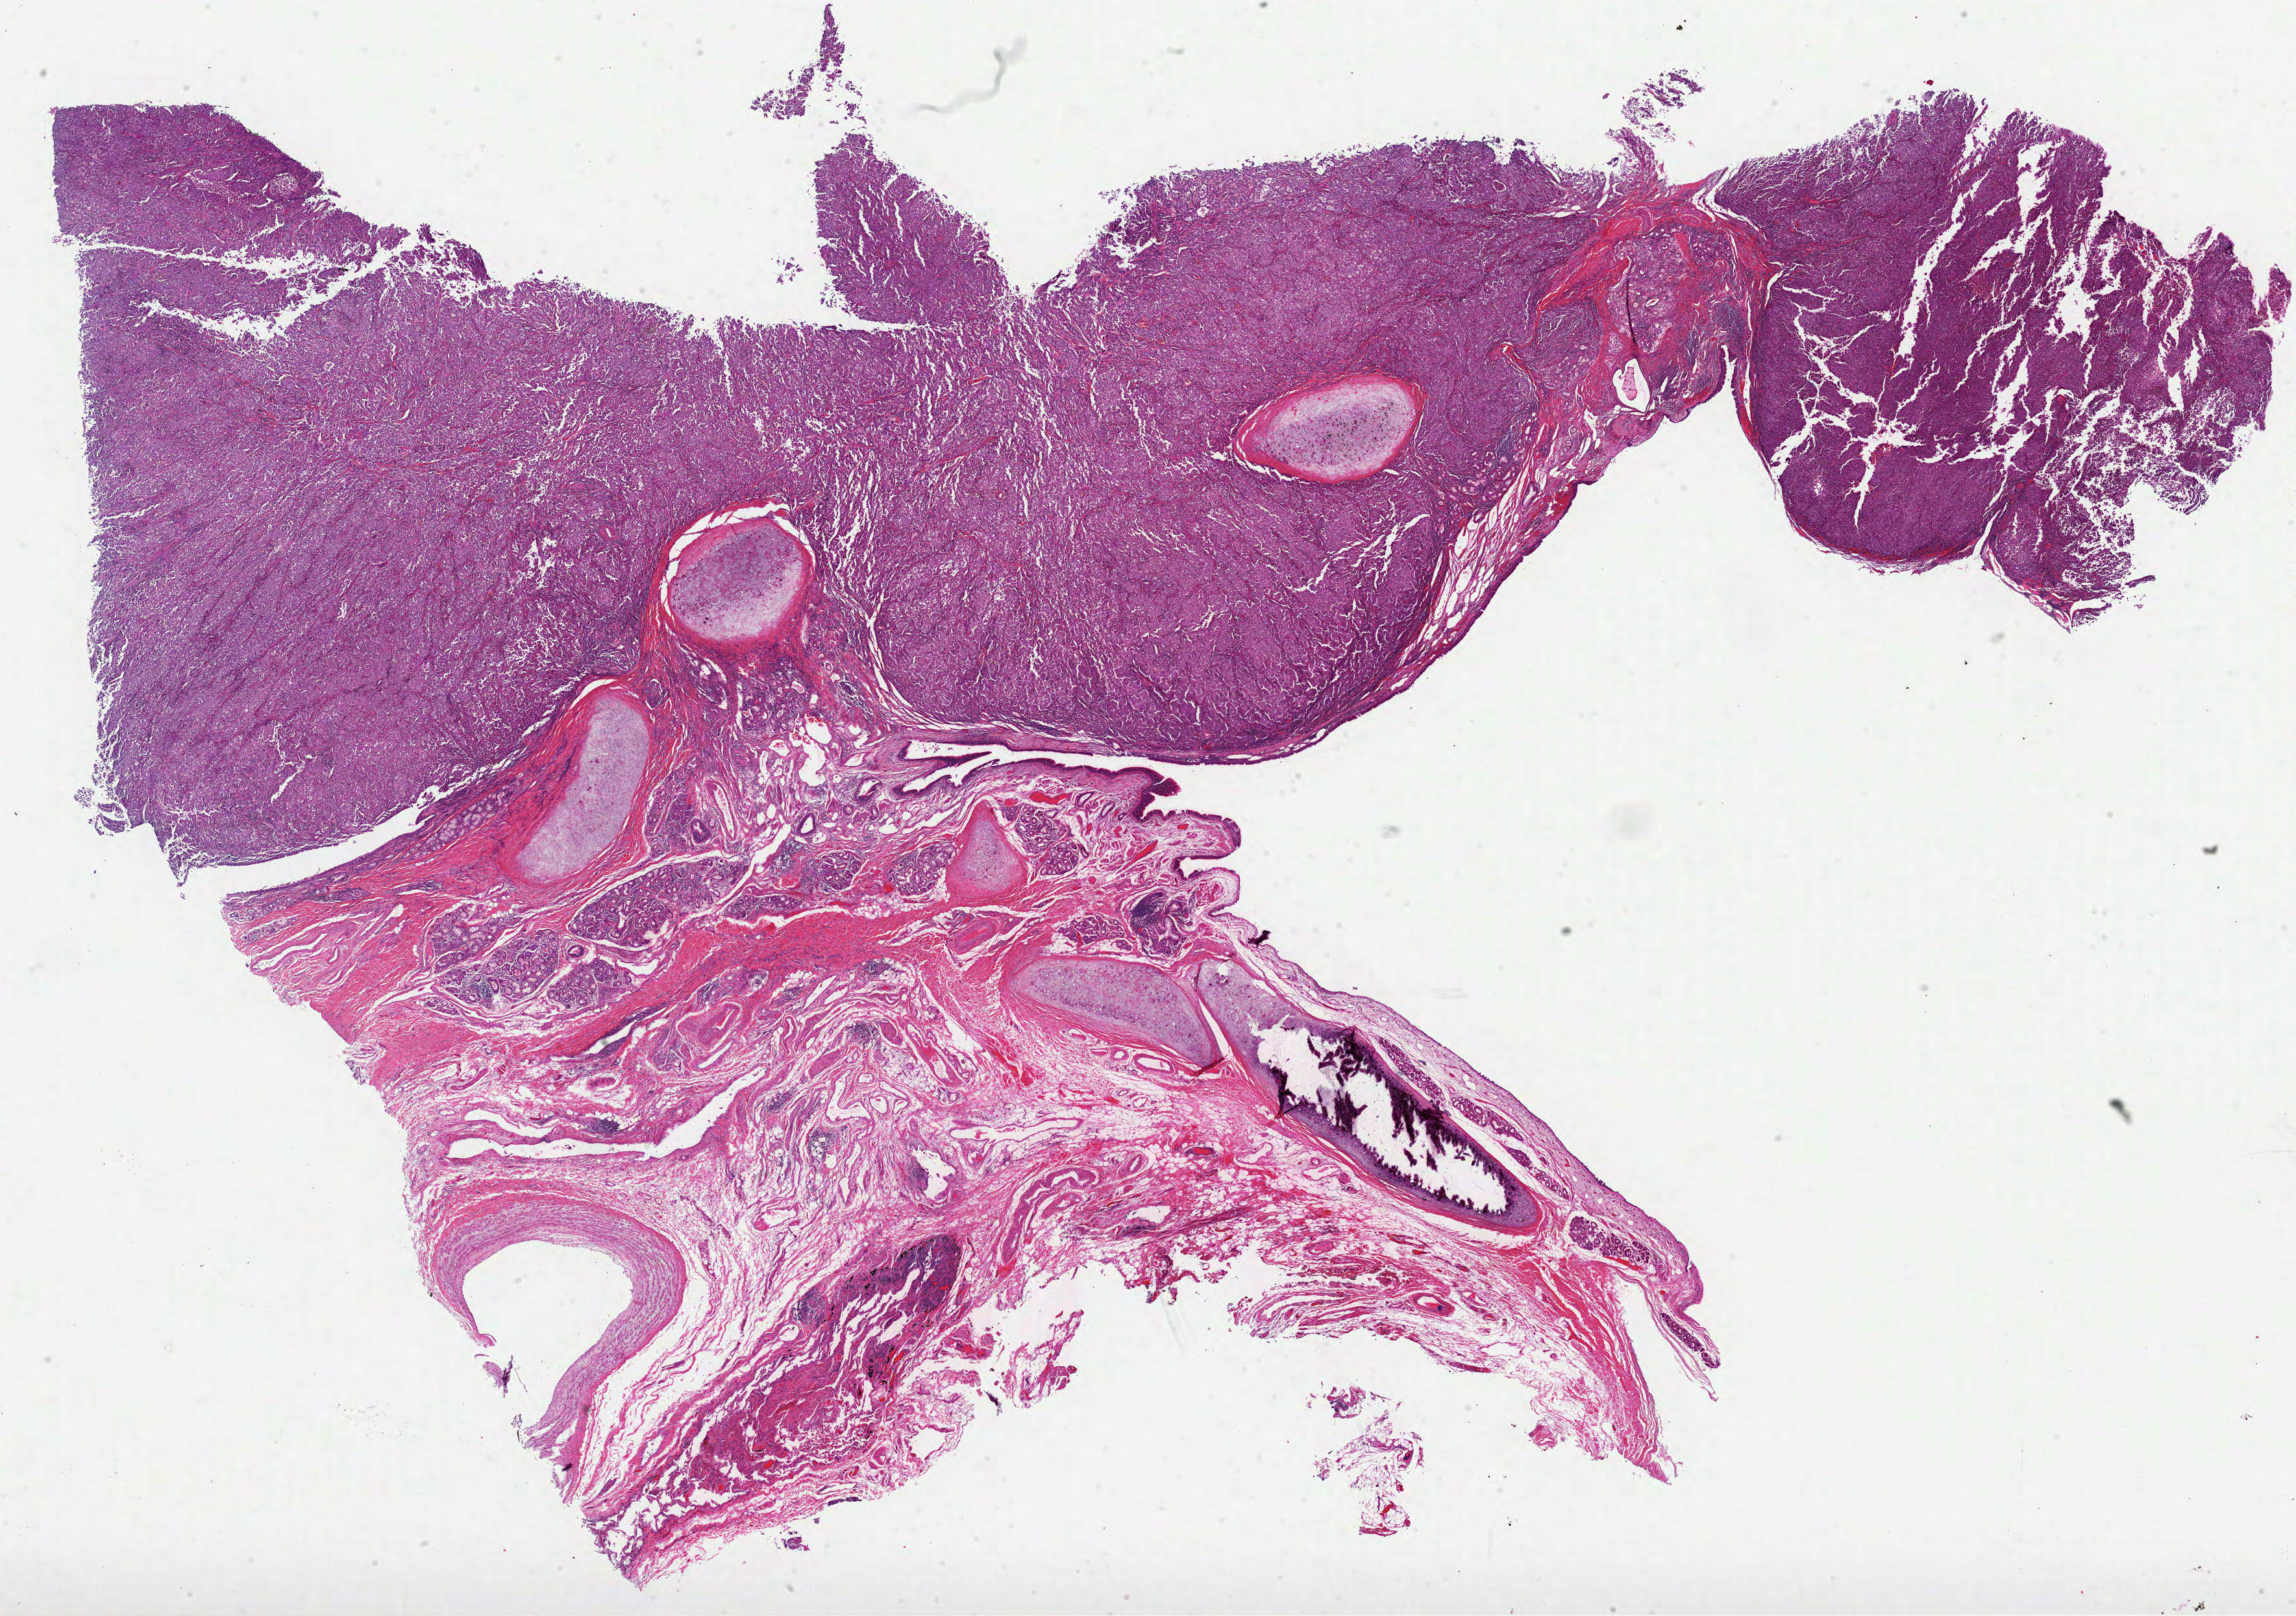
Hematoxylin and eosin (H&E) stained whole-slide image, shown as a low-resolution overview of the whole scanned area (about 28.5 x 20.1 mm, acquisition: 40x scan). Formalin-fixed paraffin-embedded (FFPE) diagnostic section. Sample: primary tumour, lung. Female, age 73 years at initial diagnosis.
AJCC pathologic stage: IIIA. Histologic diagnosis: Adenocarcinoma, NOS (main bronchus).